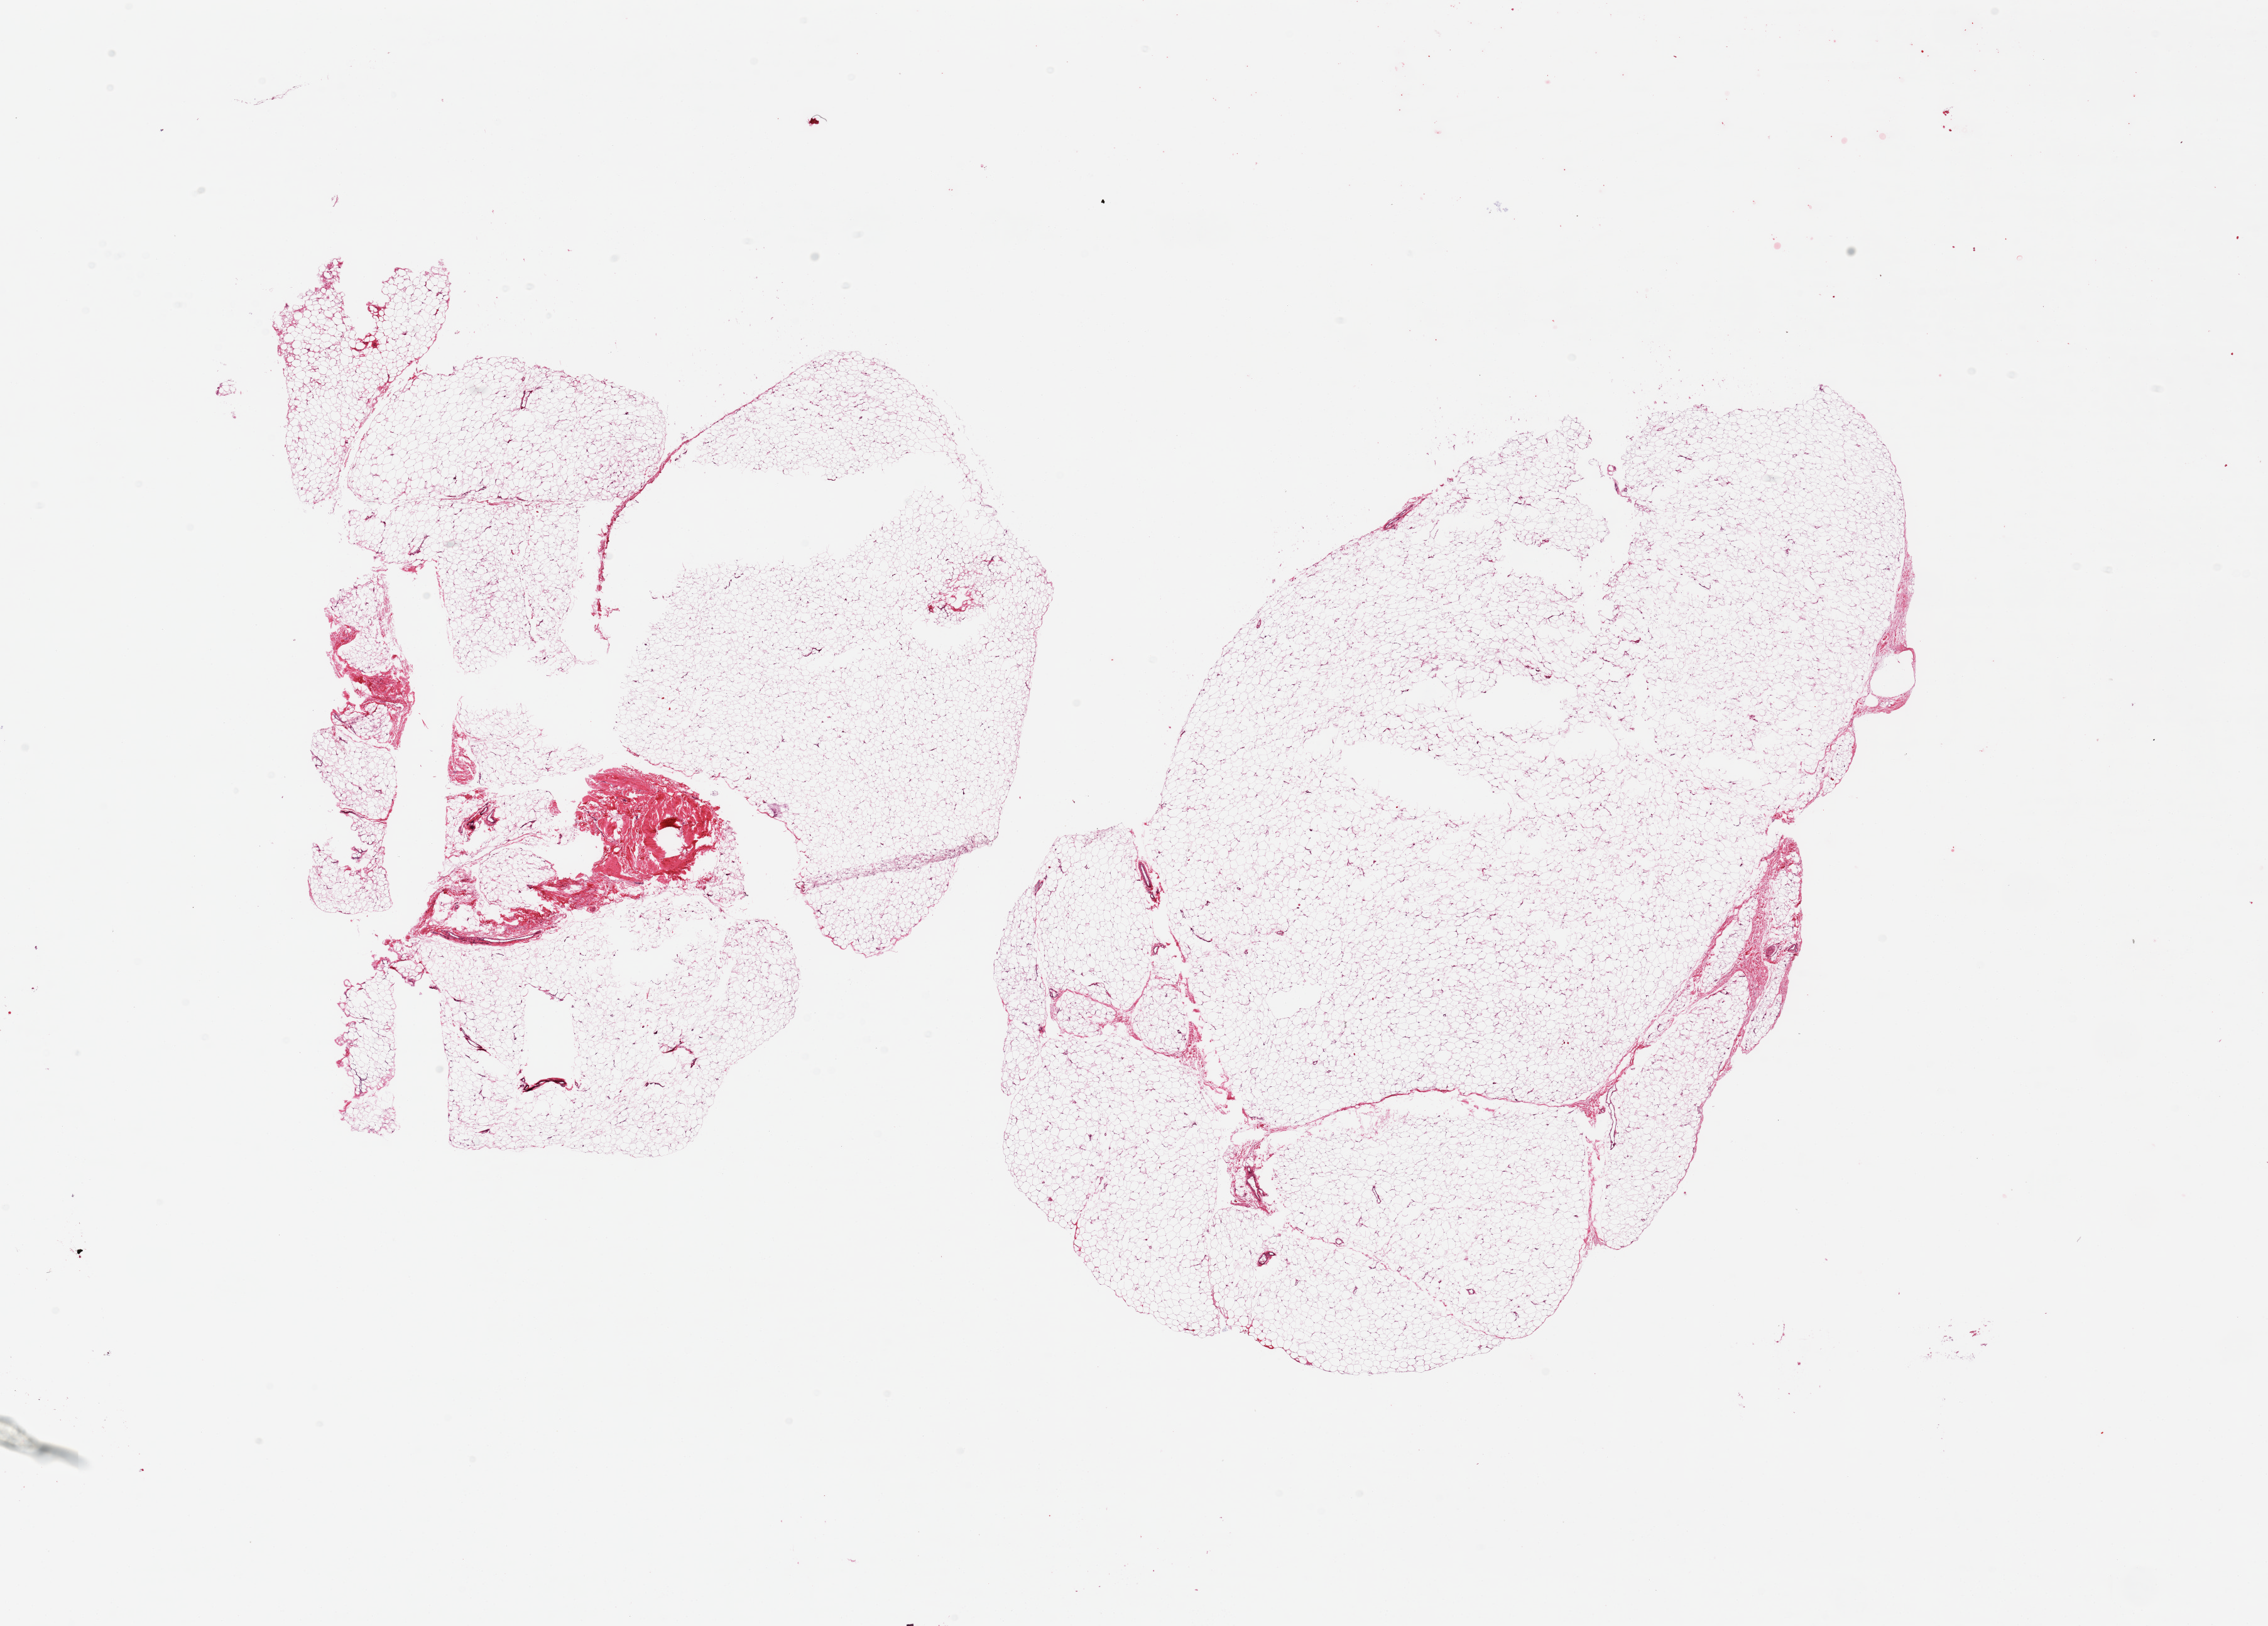
Digitized hematoxylin and eosin (H&E)-stained section, brightfield — whole scanned area (about 28.5 x 20.5 mm, from a 20x scan) shown as a low-resolution overview, PAXgene-fixed paraffin-embedded (PFPE) section, section of adipose tissue (target tissue), tissue donor sample. Donor: female.
Pathologist's review note for this sample: 2 pieces, ~5% fascia/vascular elements.